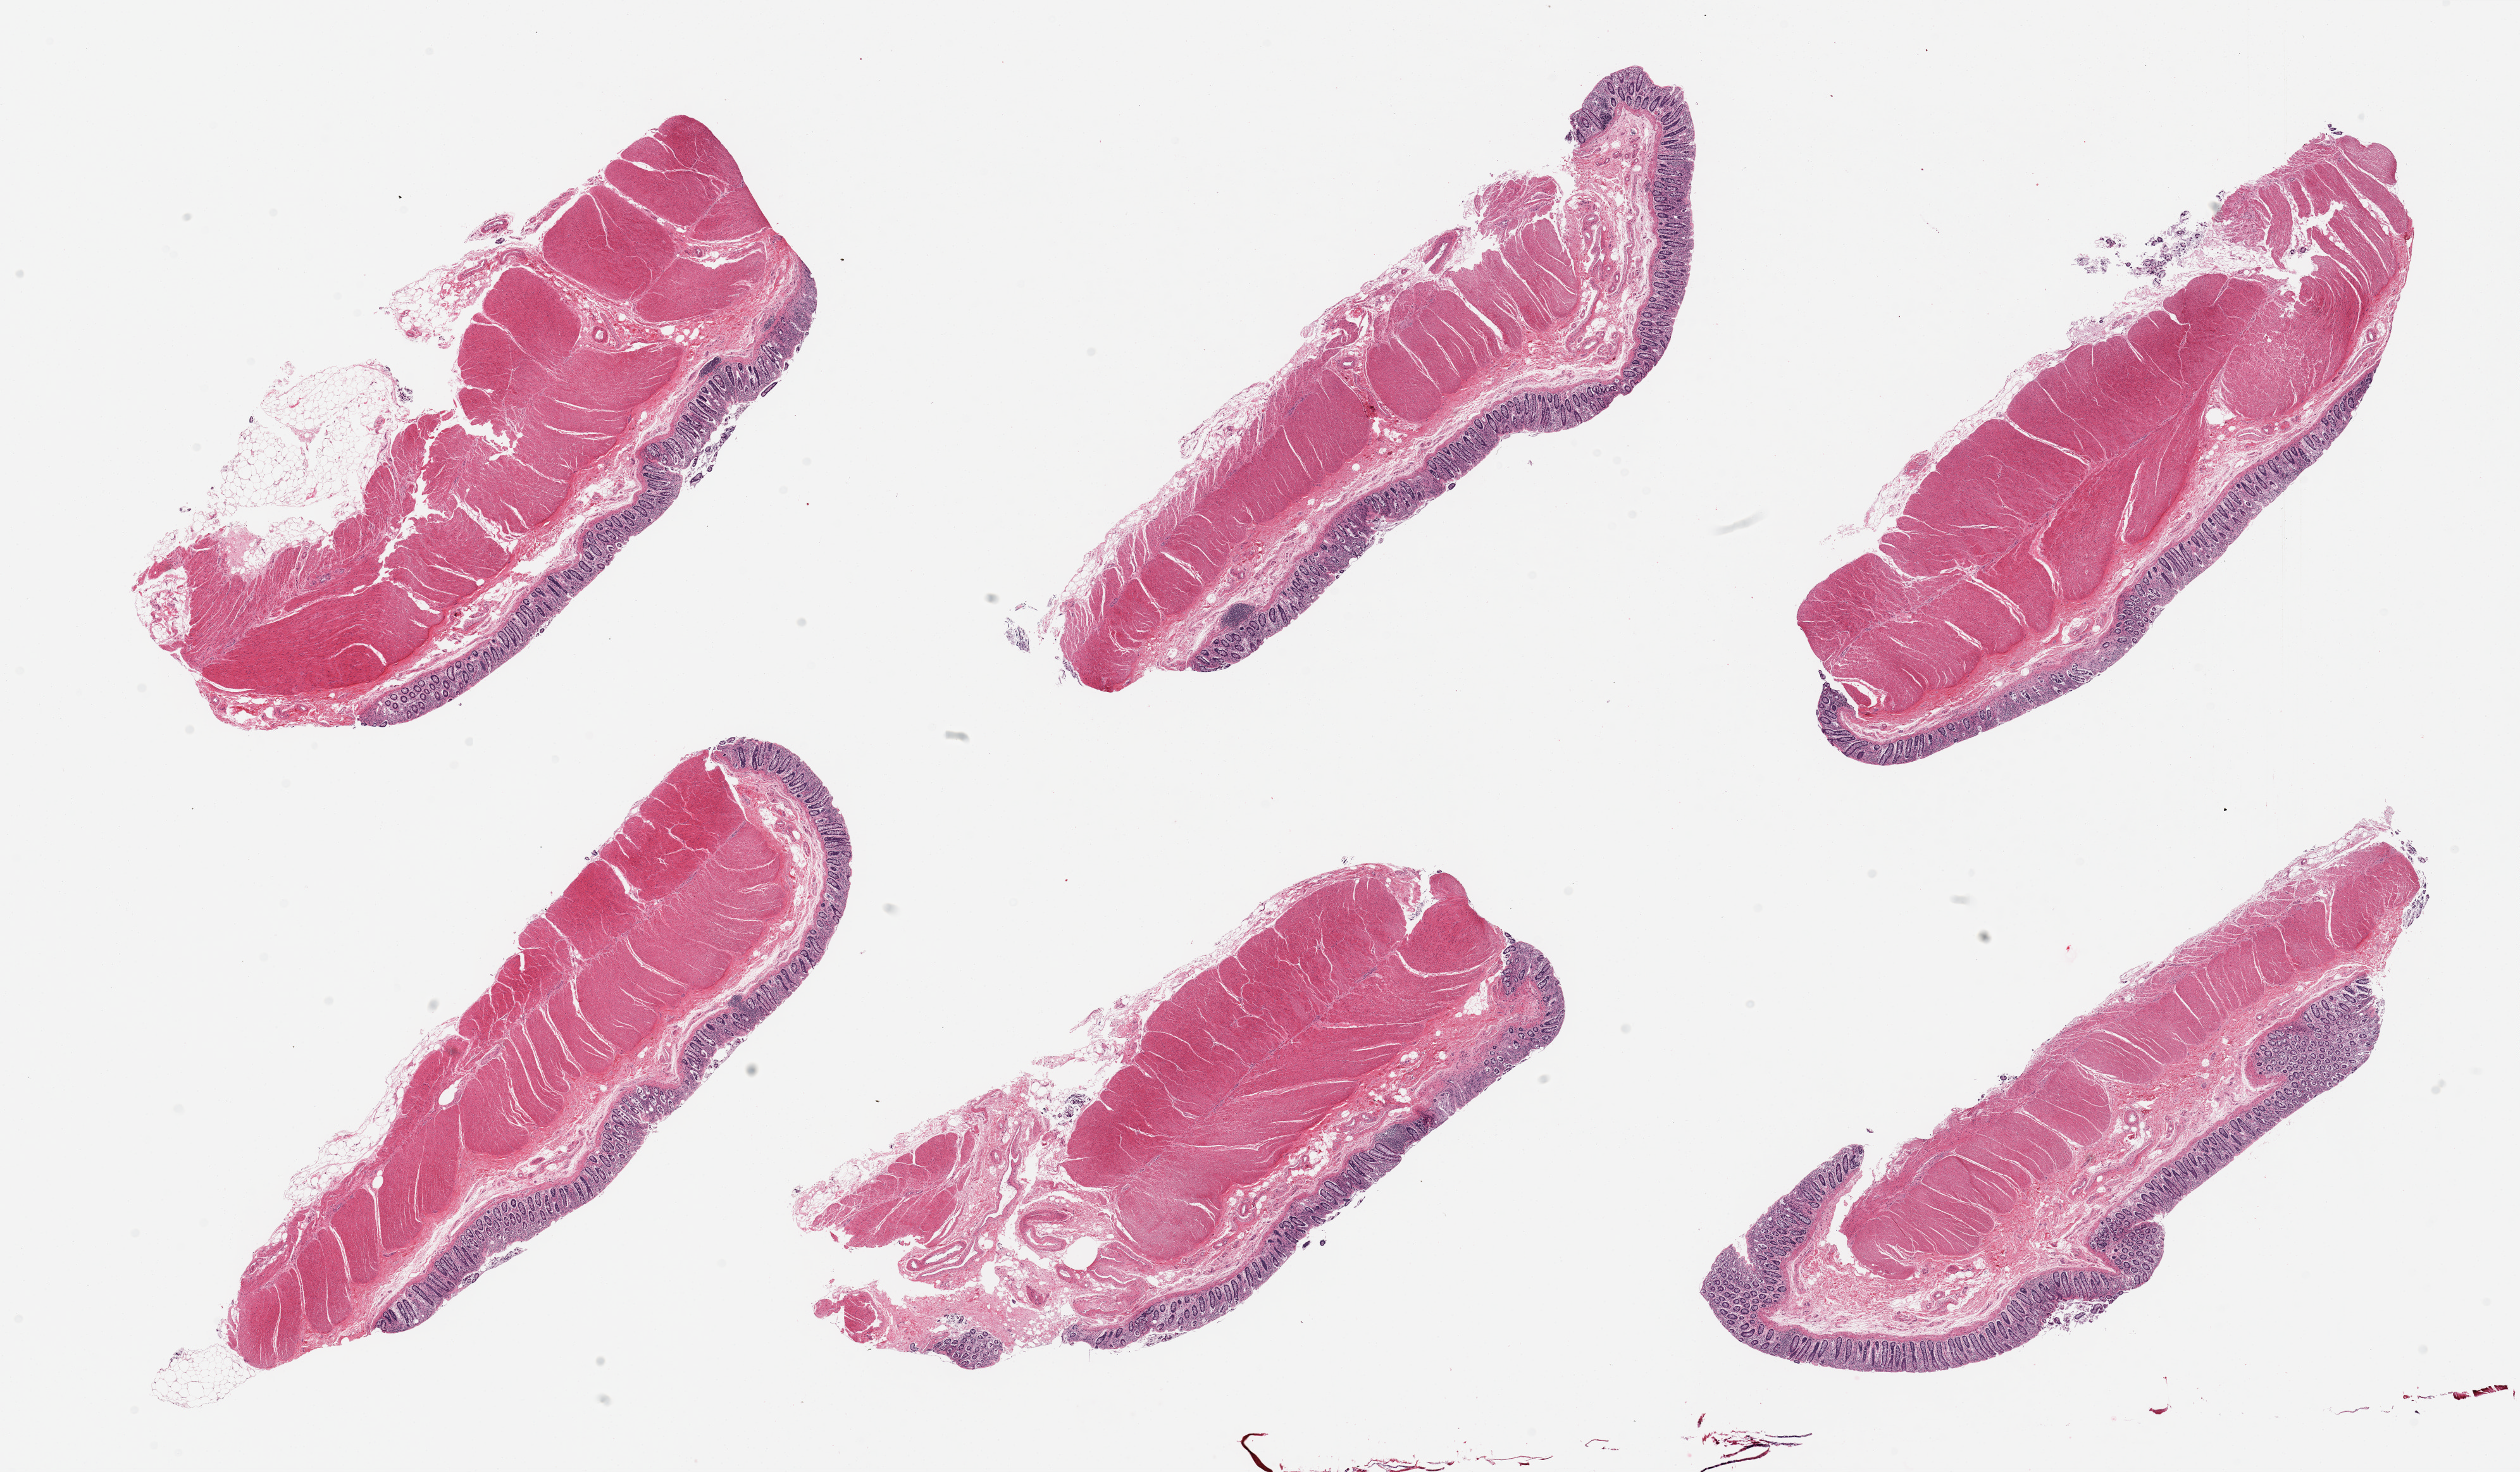
Haematoxylin and eosin whole-slide image — low-resolution overview of the scanned area, about 31.5 x 18.4 mm (slide scanned at 20x). PAXgene-fixed paraffin-embedded (PFPE) section. Sampled site (target tissue): sigmoid colon. Donor tissue sample.
Reviewer comment on this tissue sample: 6 pieces, ~90% muscularis, 'contaminant' mucosa in all sections.